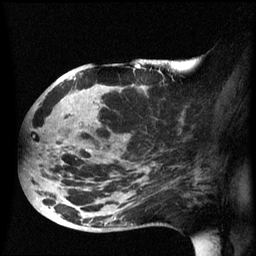
Breast MRI (dynamic contrast-enhanced), one sagittal slice; slice 29 of 60 in the series (ordered by position); dynamic contrast-enhanced series, image 2 of 3 at this slice position (ordered by acquisition); 1.5 T; TE 4.2 ms, TR 8.4 ms; 2.5 mm slice thickness; 256 × 256 image matrix, field of view 220 × 220 mm. Female patient, age 49 years.
Structures marked on this image (semi-automatically segmented with operator editing):
- analysis volume of interest (the breast-tissue region the enhancement analysis was run in; not a lesion): bounding box [x1, y1, x2, y2] px = [24, 72, 185, 233]
- tumour enhancement mask (voxels above the 70 % enhancement threshold inside the analysis volume of interest): [49, 78, 88, 225]